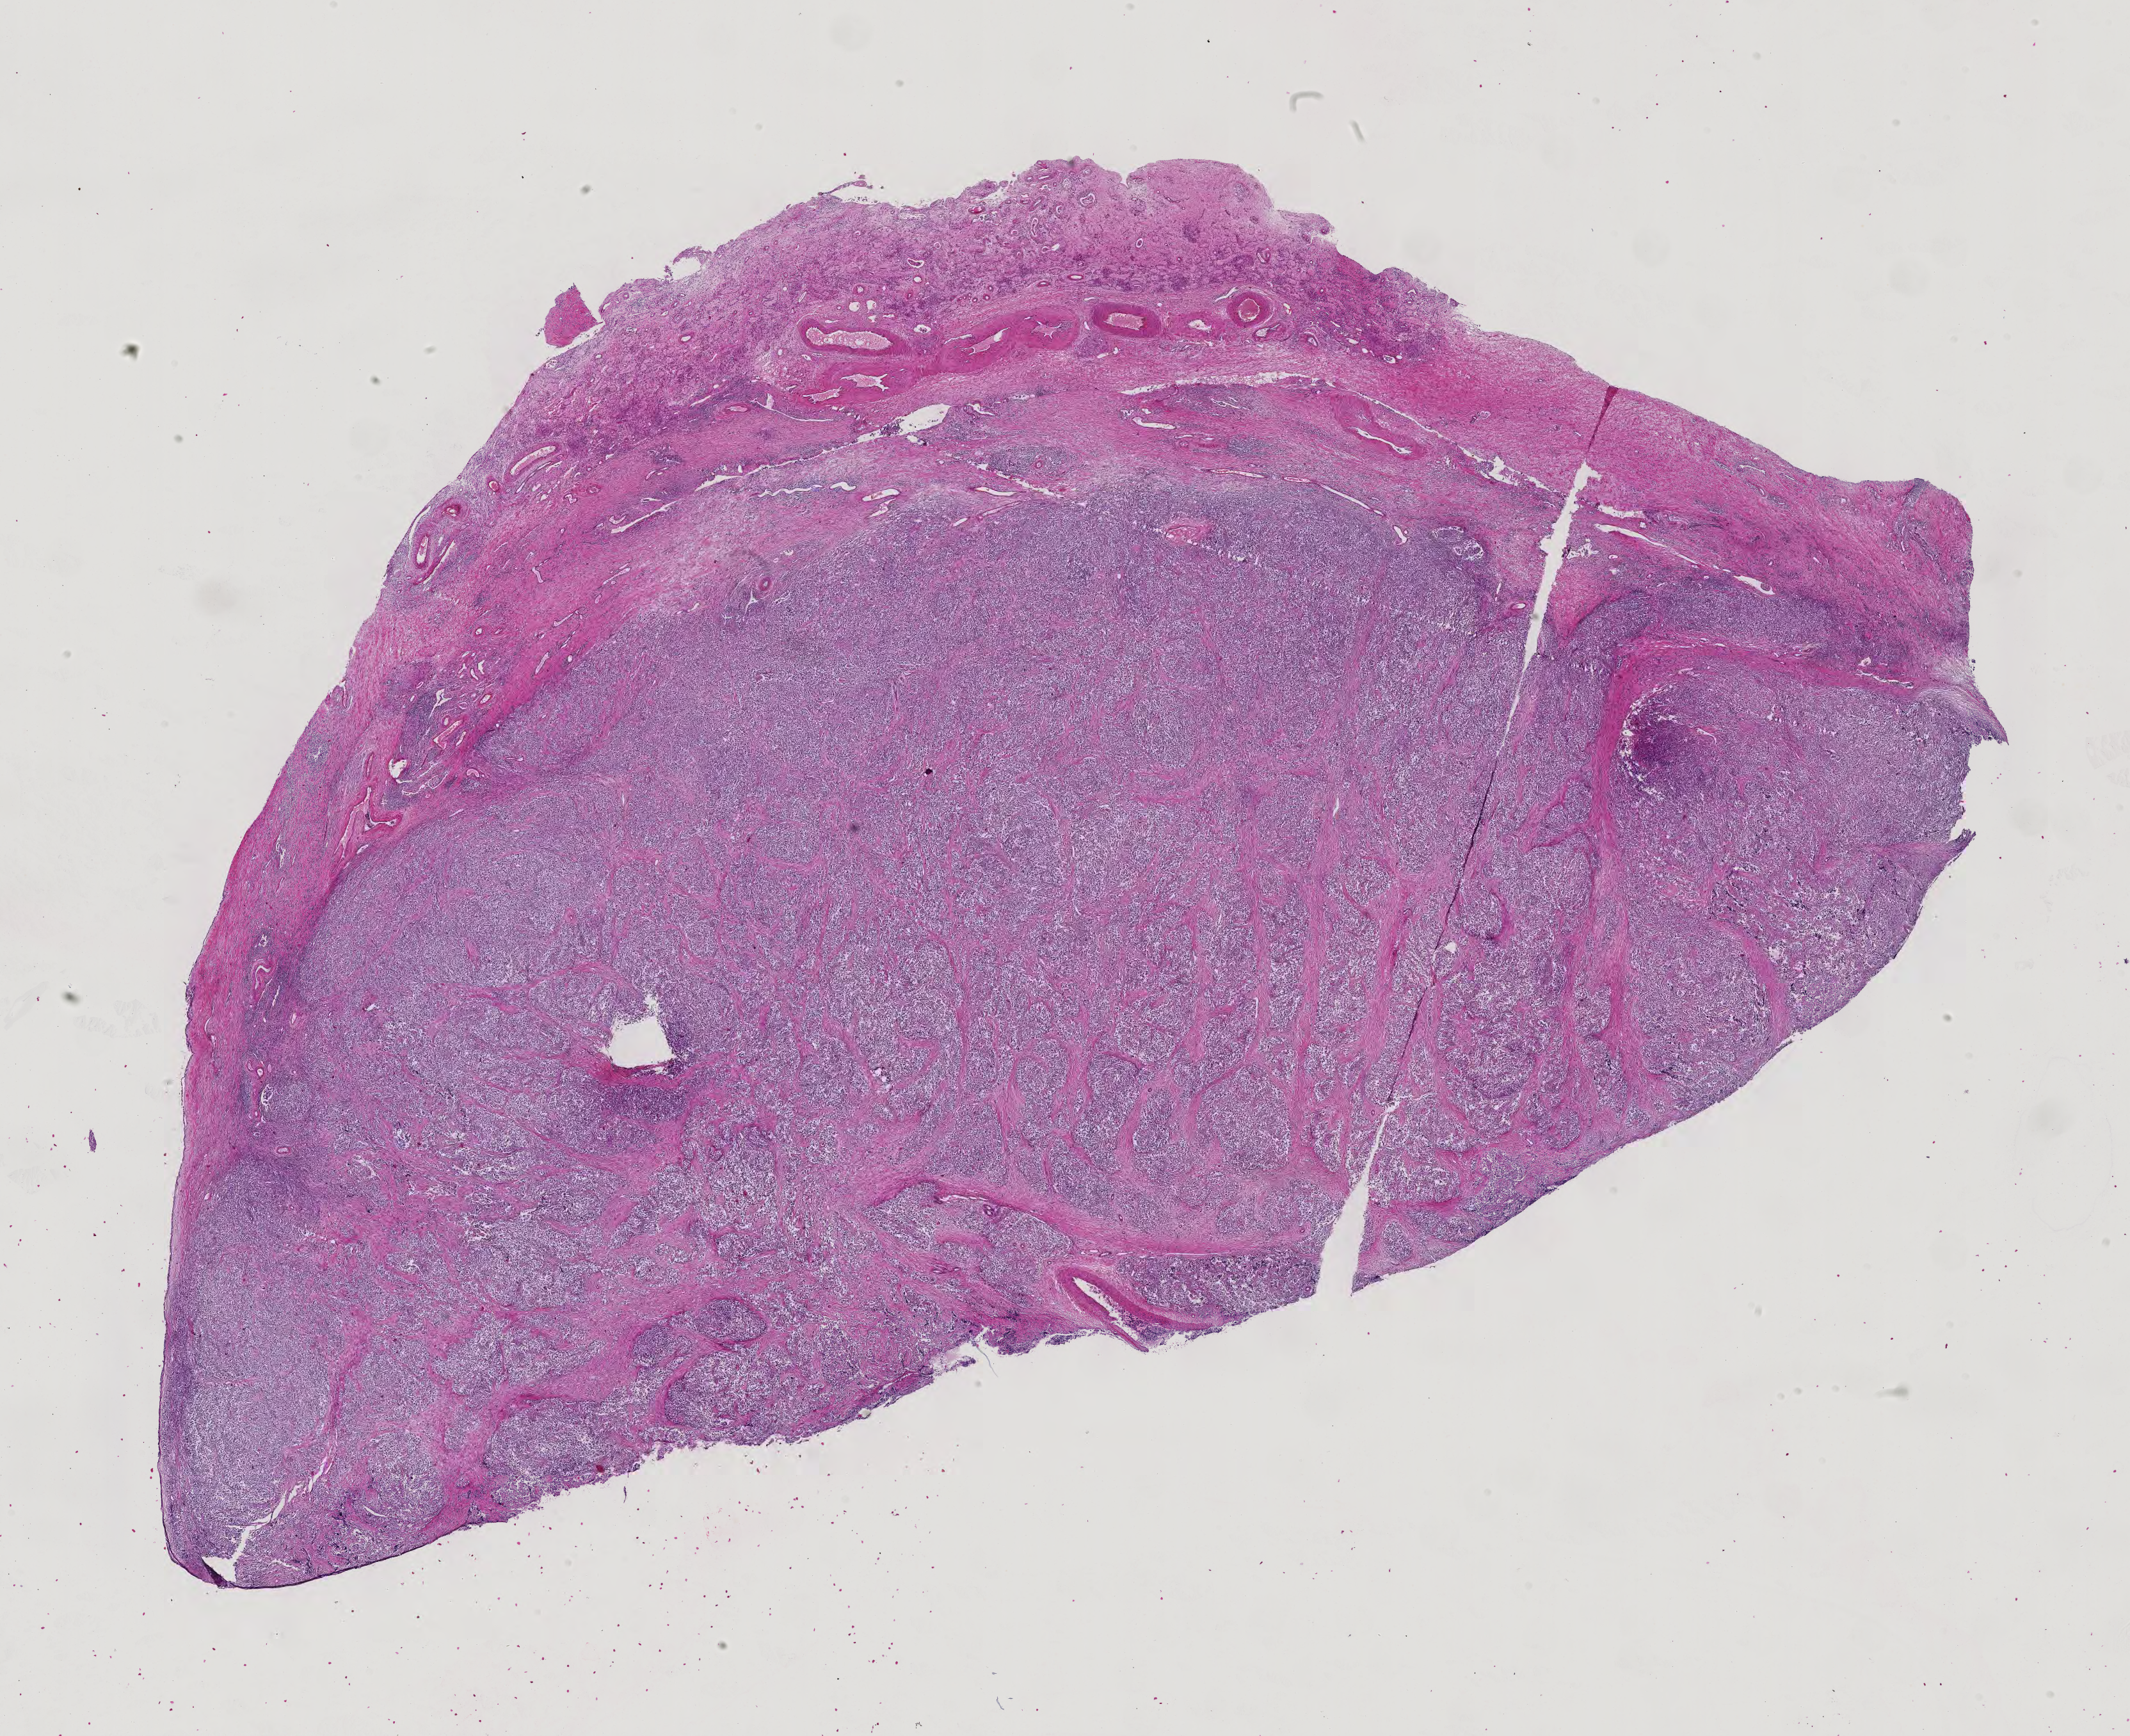
Digitized H&E tissue section (whole slide), whole scanned area (about 24.2 x 19.8 mm, acquisition: 40x scan) shown as a low-resolution overview, formalin-fixed paraffin-embedded (FFPE) diagnostic section, primary tumour sample from the testis. Male, age 30 years at initial diagnosis.
• laterality: right
• histologic diagnosis: Seminoma, NOS
• AJCC pathologic stage: IS